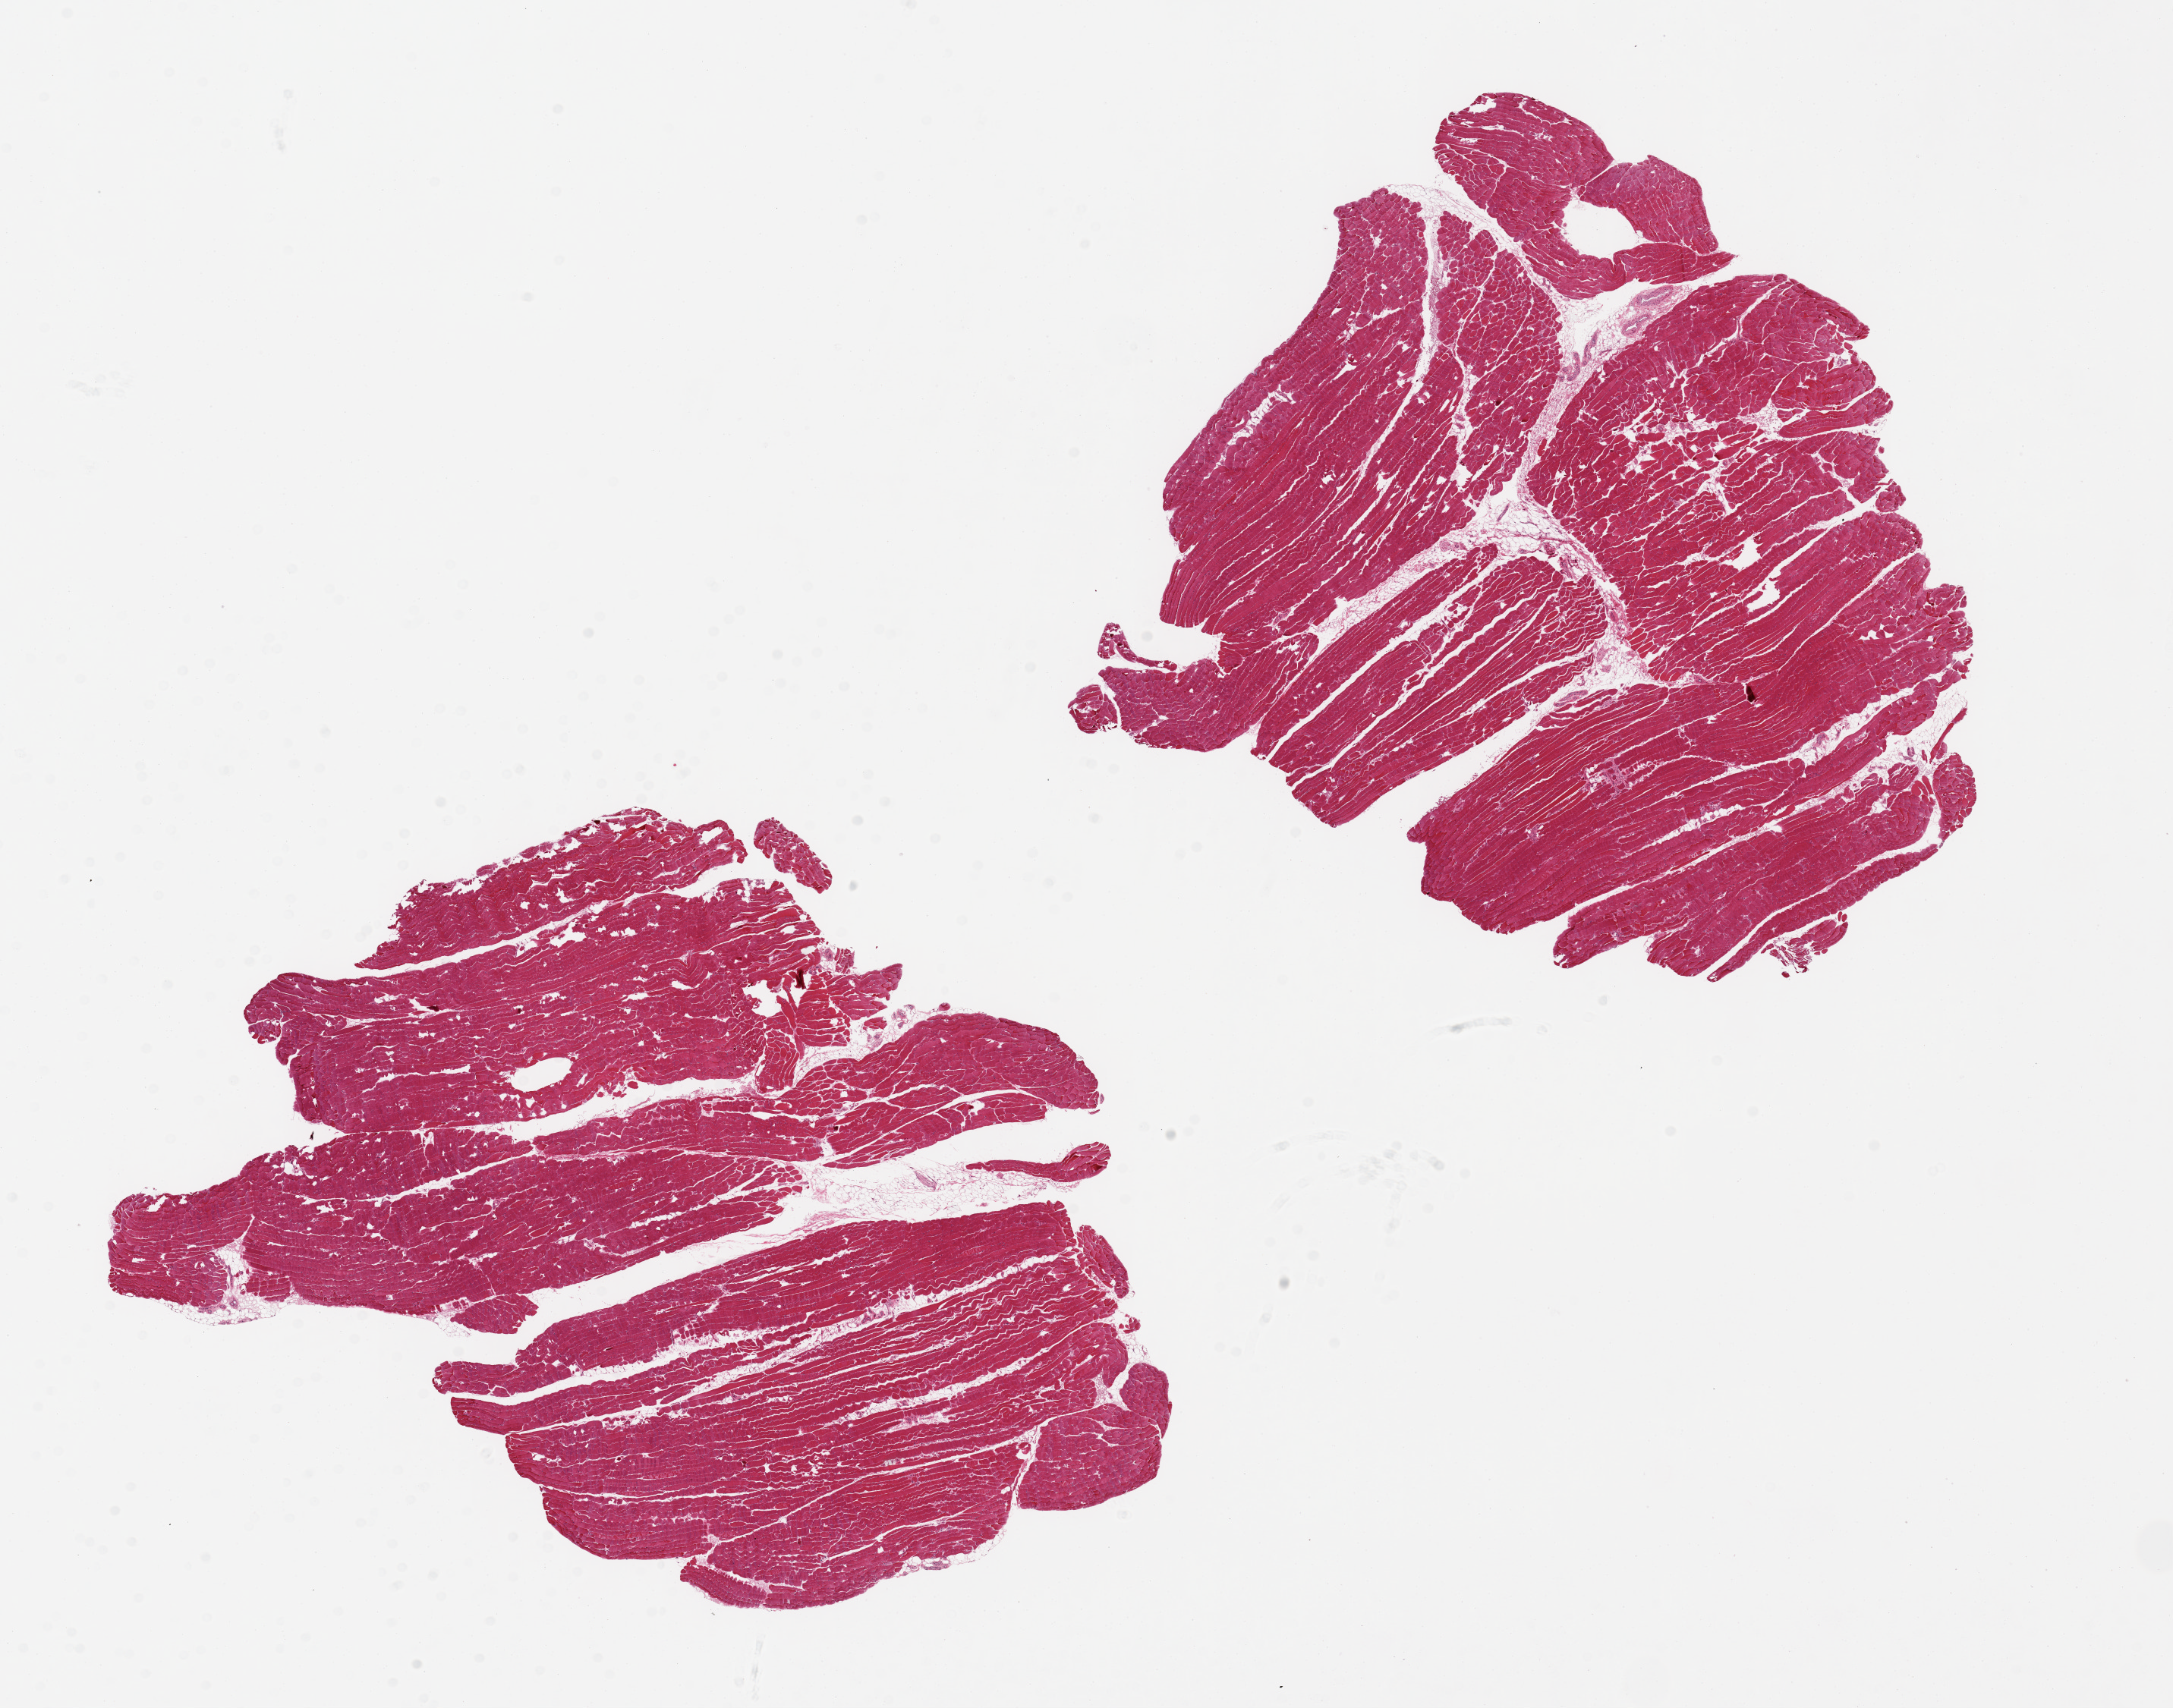
Whole-slide image, hematoxylin and eosin (H&E) stain, brightfield — a low-resolution overview of the entire scanned area, about 22.6 x 17.8 mm (from a 20x scan). PAXgene-fixed paraffin-embedded (PFPE) section. Sampled site (target tissue): skeletal muscle. Tissue donor sample. Female donor.
Review note (as recorded): 2 pieces, 10x9 & 9.5x9mm; <5% interstitial fat.